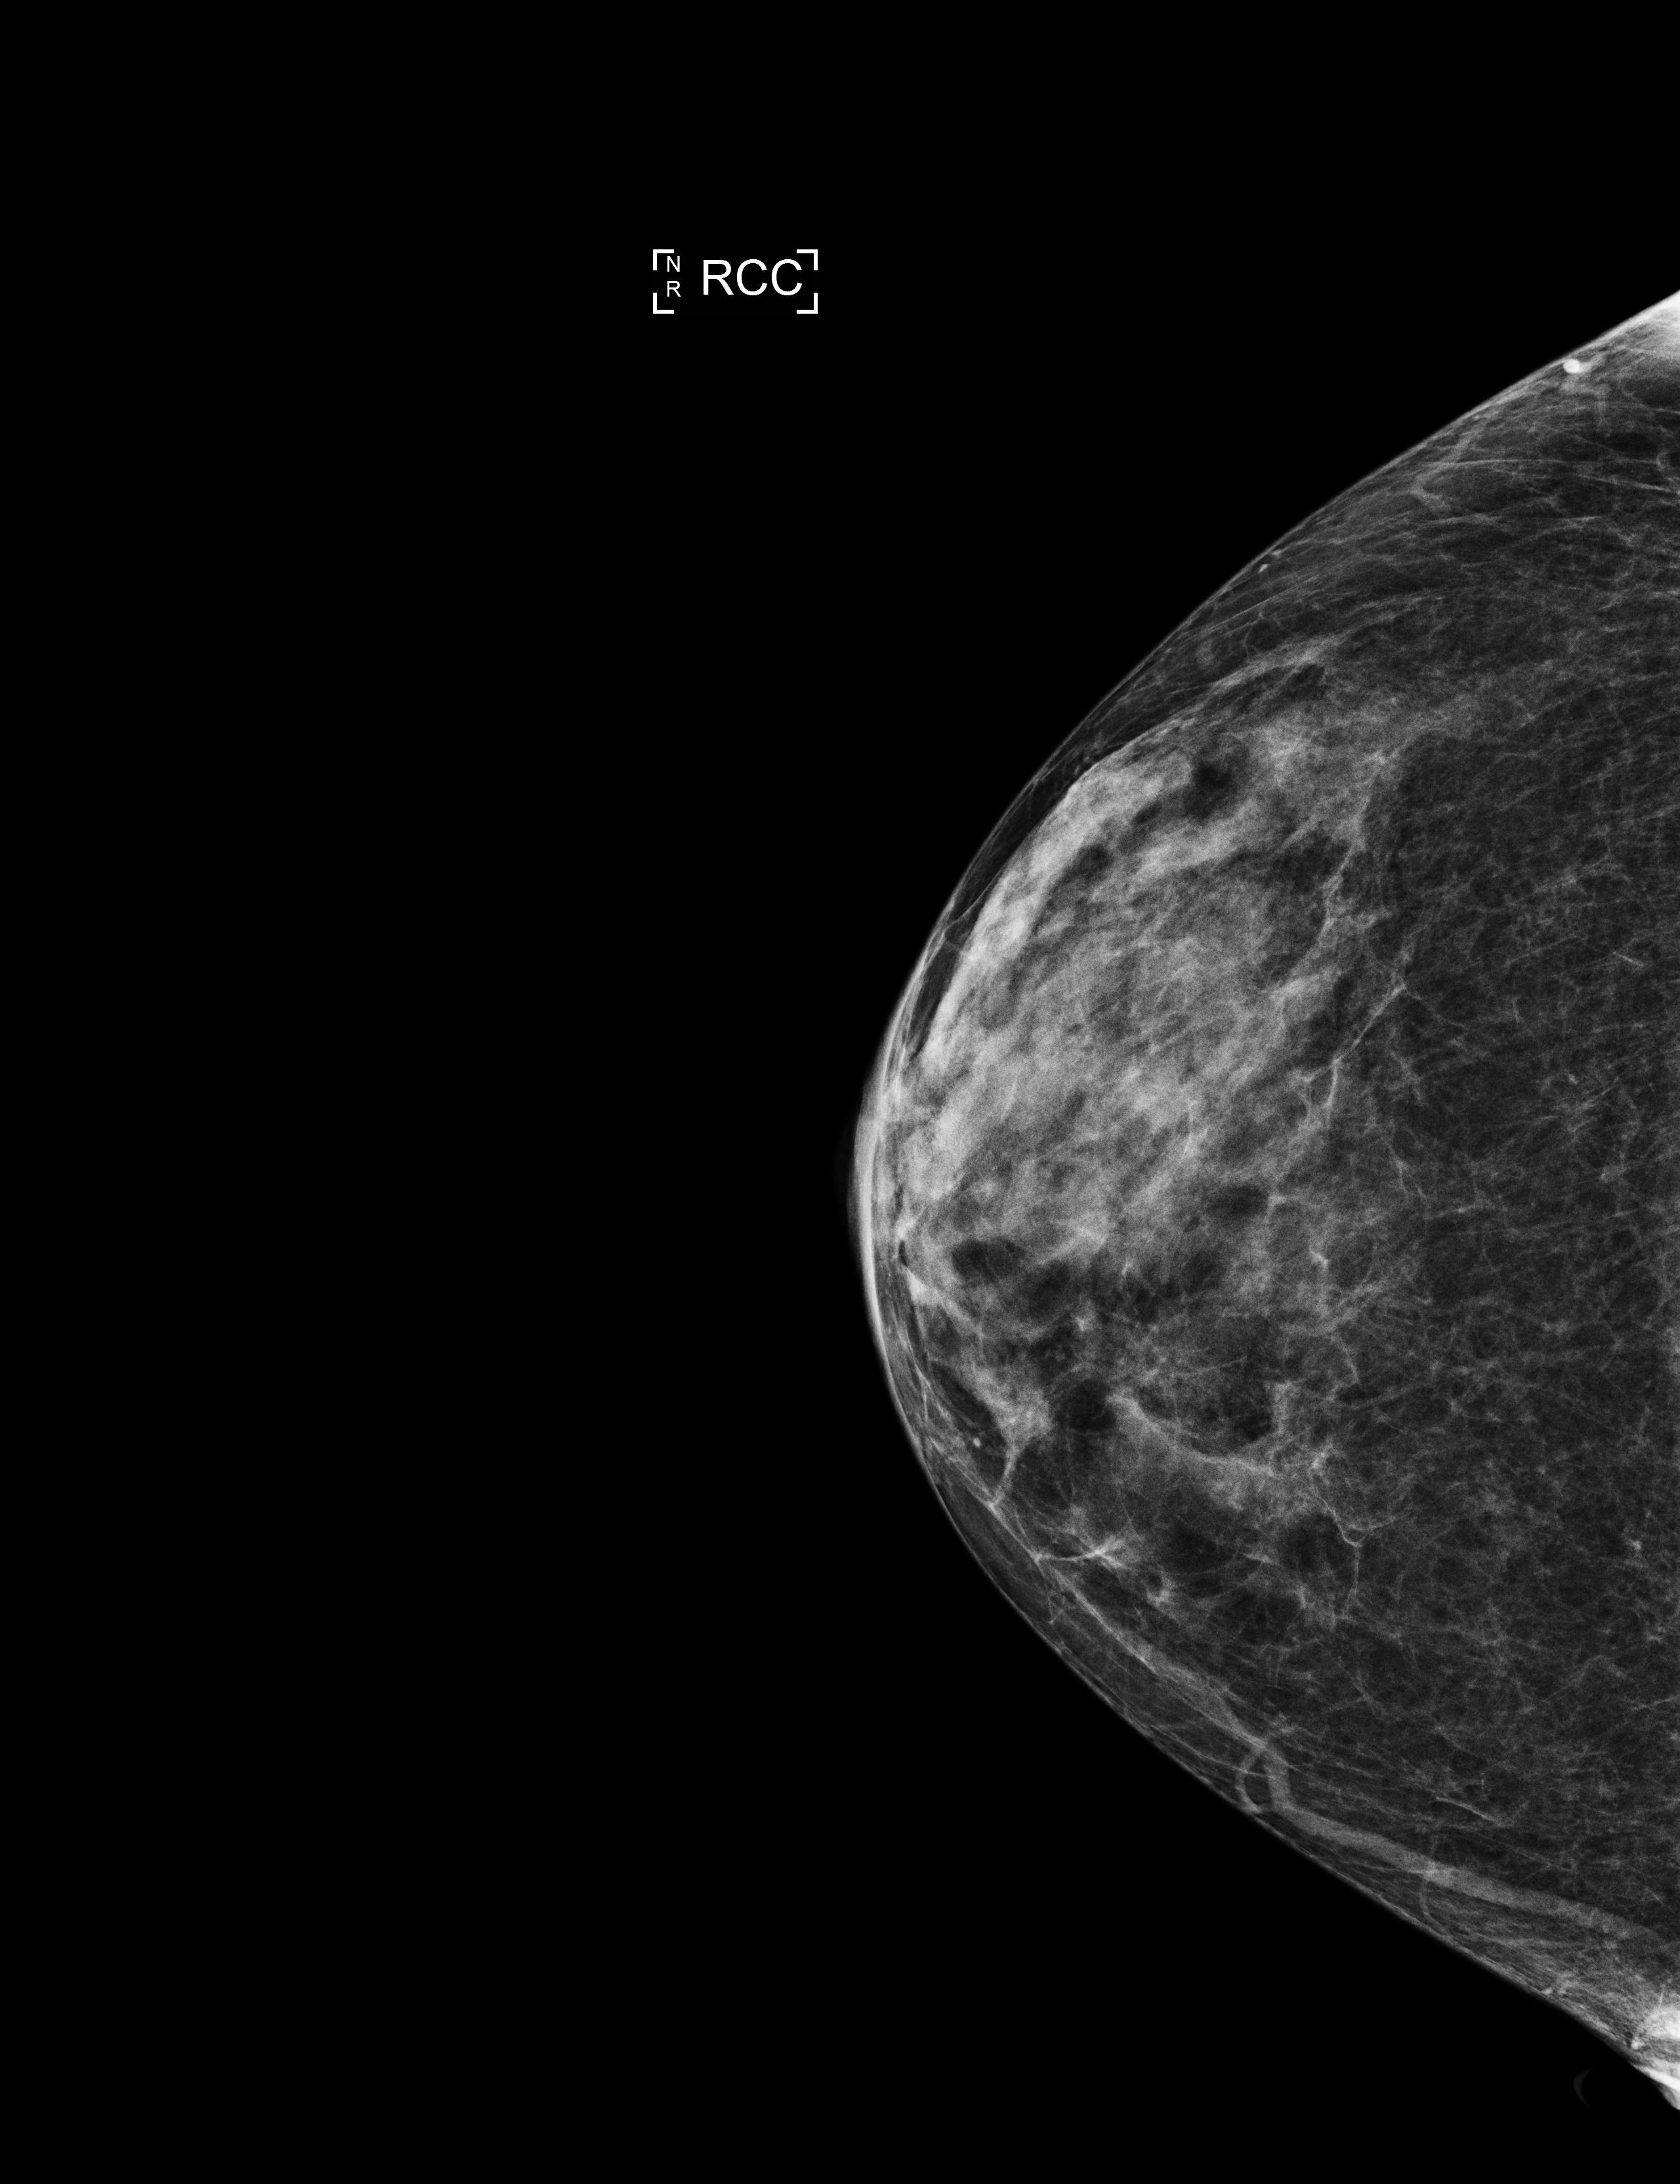
Full-field digital mammogram (FFDM); right breast; craniocaudal (CC) view; annual screening mammography examination; compressed breast thickness 28 mm; system: Selenia Dimensions. Patient aged 59 years (female).
- BI-RADS breast density category at the screening exam (both breasts, scale 1–4): 2
- final BI-RADS assessment for this screening round (tomosynthesis exam, both breasts): category 1
- recall: no recall after this screen